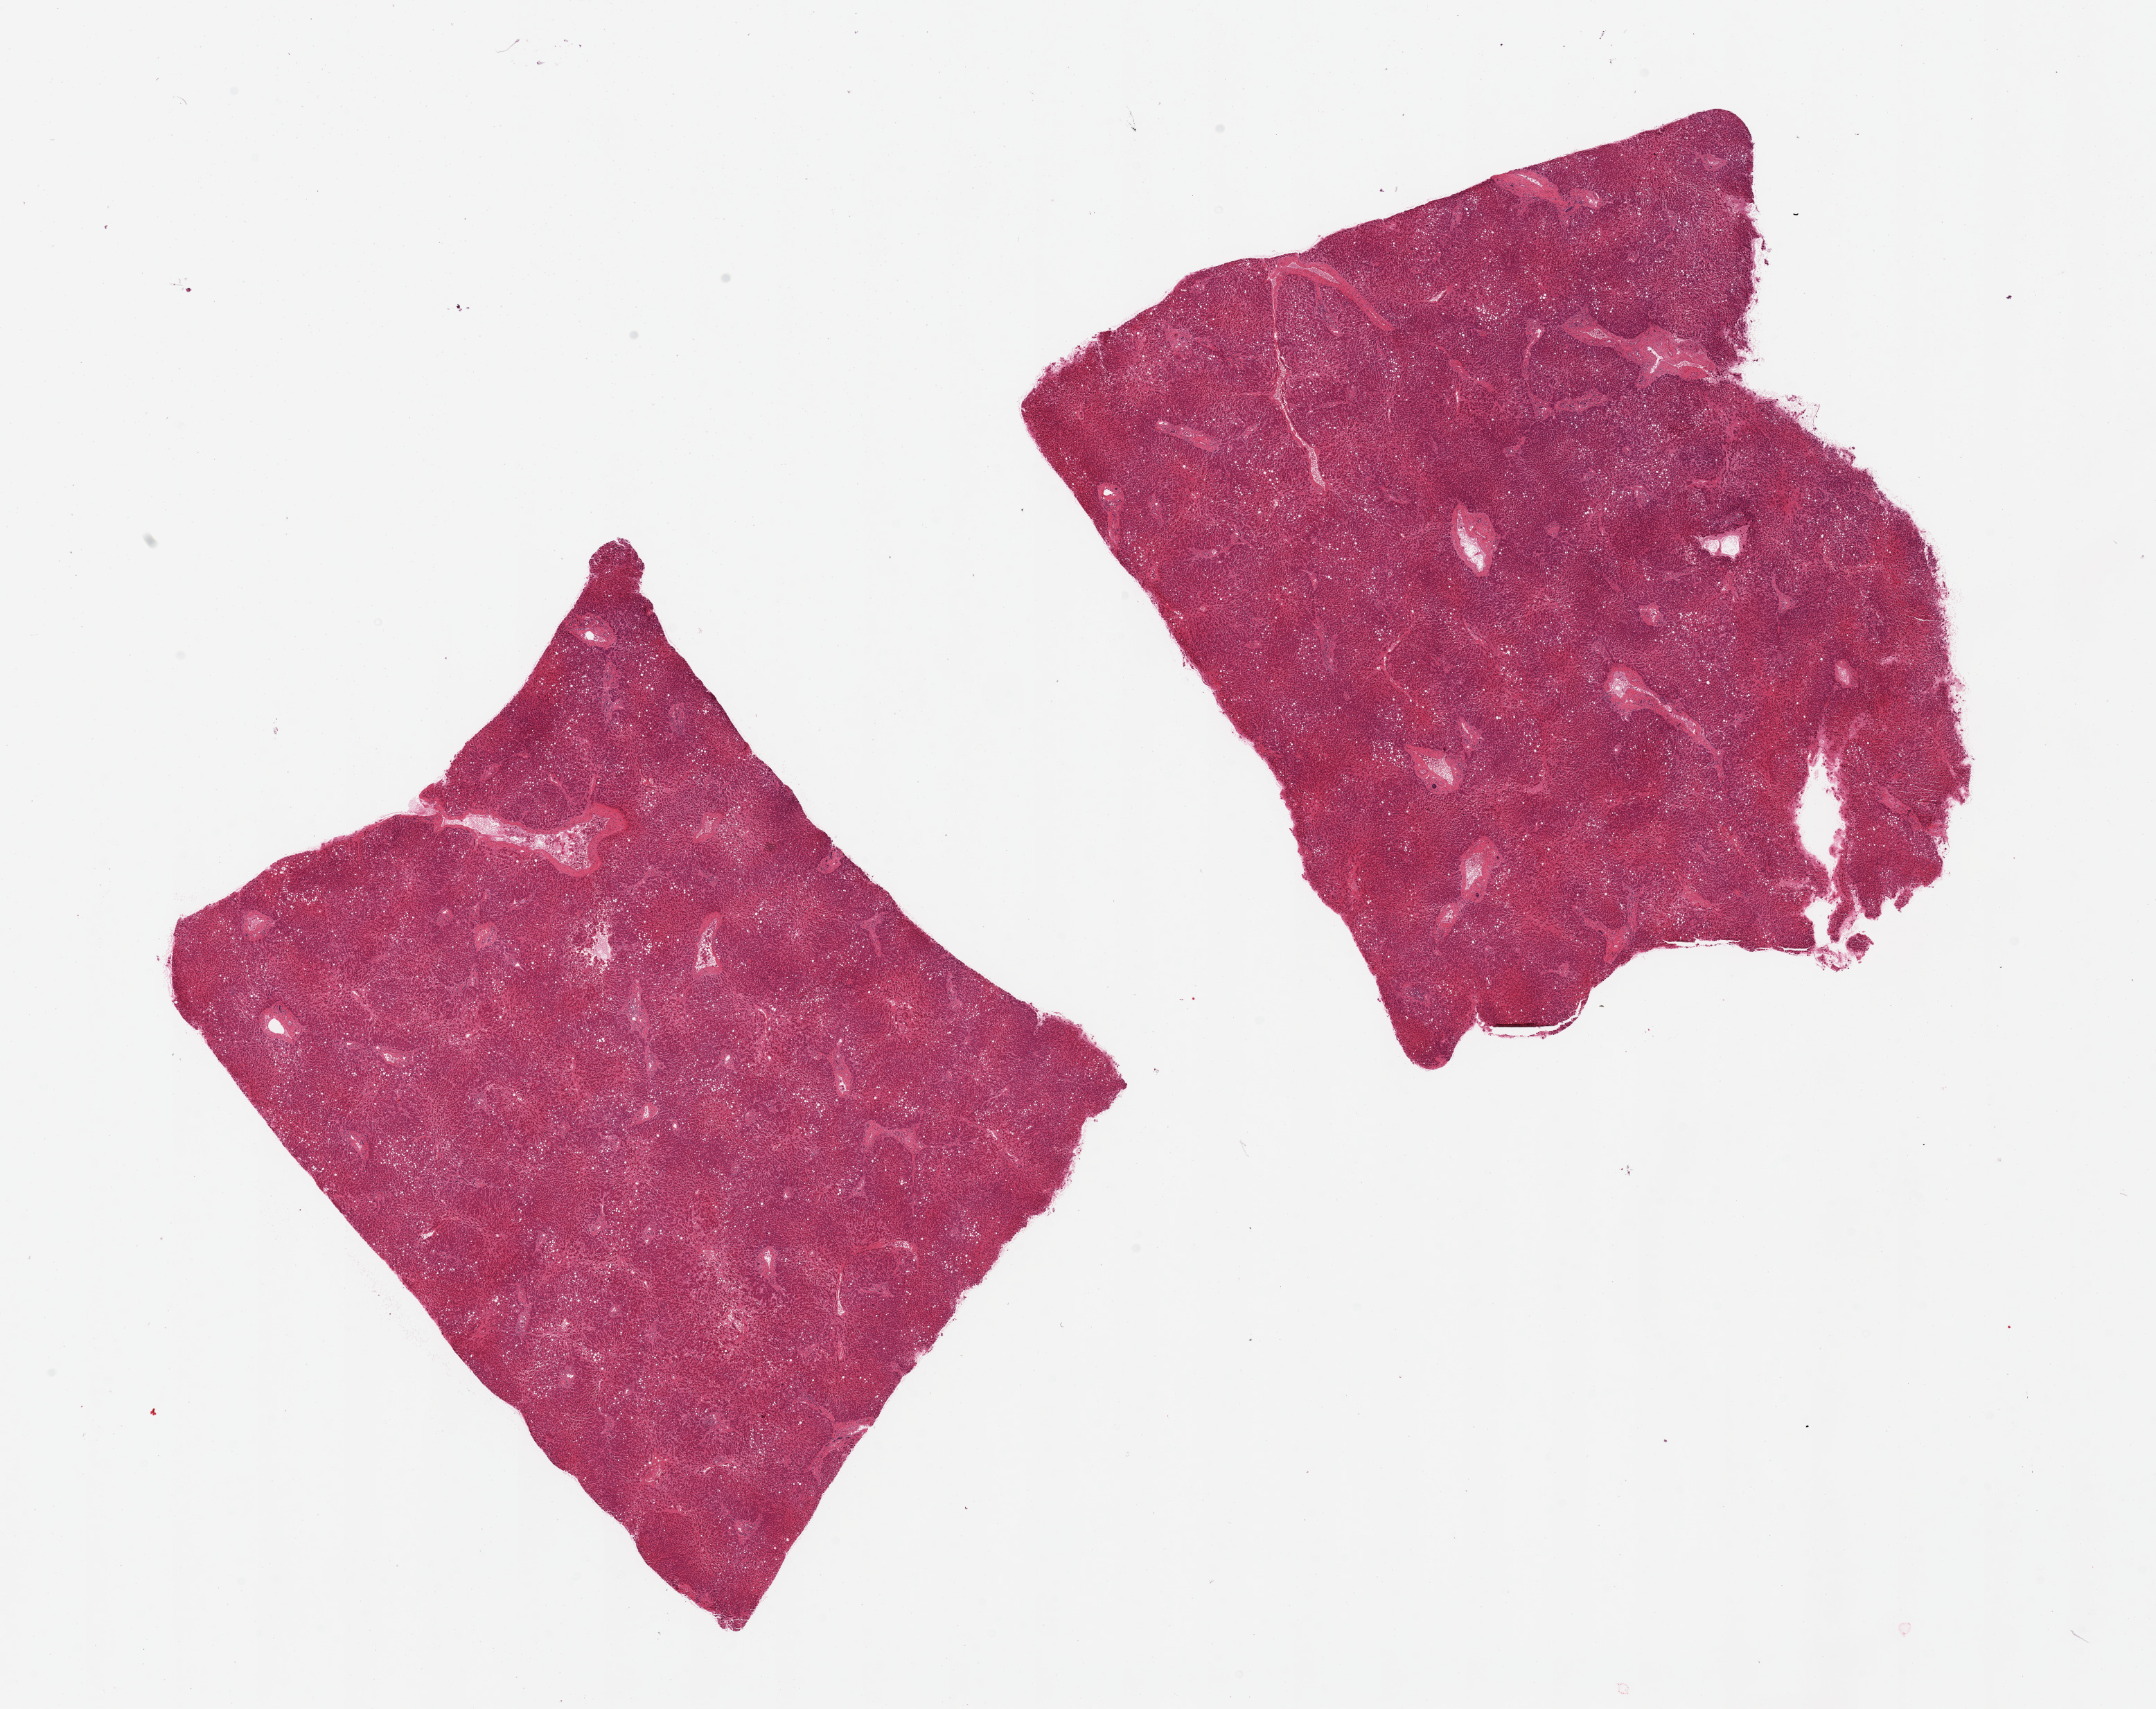
Hematoxylin and eosin (H&E) whole-slide image, brightfield, a low-resolution overview of the entire scanned area, about 24.6 x 19.5 mm; PAXgene-fixed paraffin-embedded (PFPE) section; target tissue: liver; tissue donor sample.
• pathologist's review note for this sample: 2 pieces diffuse mild macrovesciular steatosis involves ~20% of parenchyma